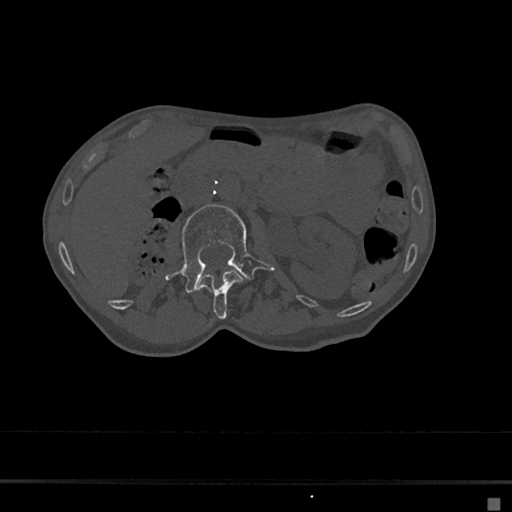
CT including the spine, one axial slice; slice 30 of 797 in the series (ordered by position); reconstruction kernel Br40s/3; 120 kVp; bone window (W 1800 / L 400 HU); 0.5 mm slice thickness; 512 × 512 image matrix. Female patient, age 68 years. From the clinical record (not read from this slice): primary cancer: renal.
Annotated regions visible in this slice (semi-automatically segmented with operator editing):
- L1 vertebra: bounding box [x1, y1, x2, y2] px = [196, 269, 243, 319]
- L2 vertebra: [165, 204, 274, 292]